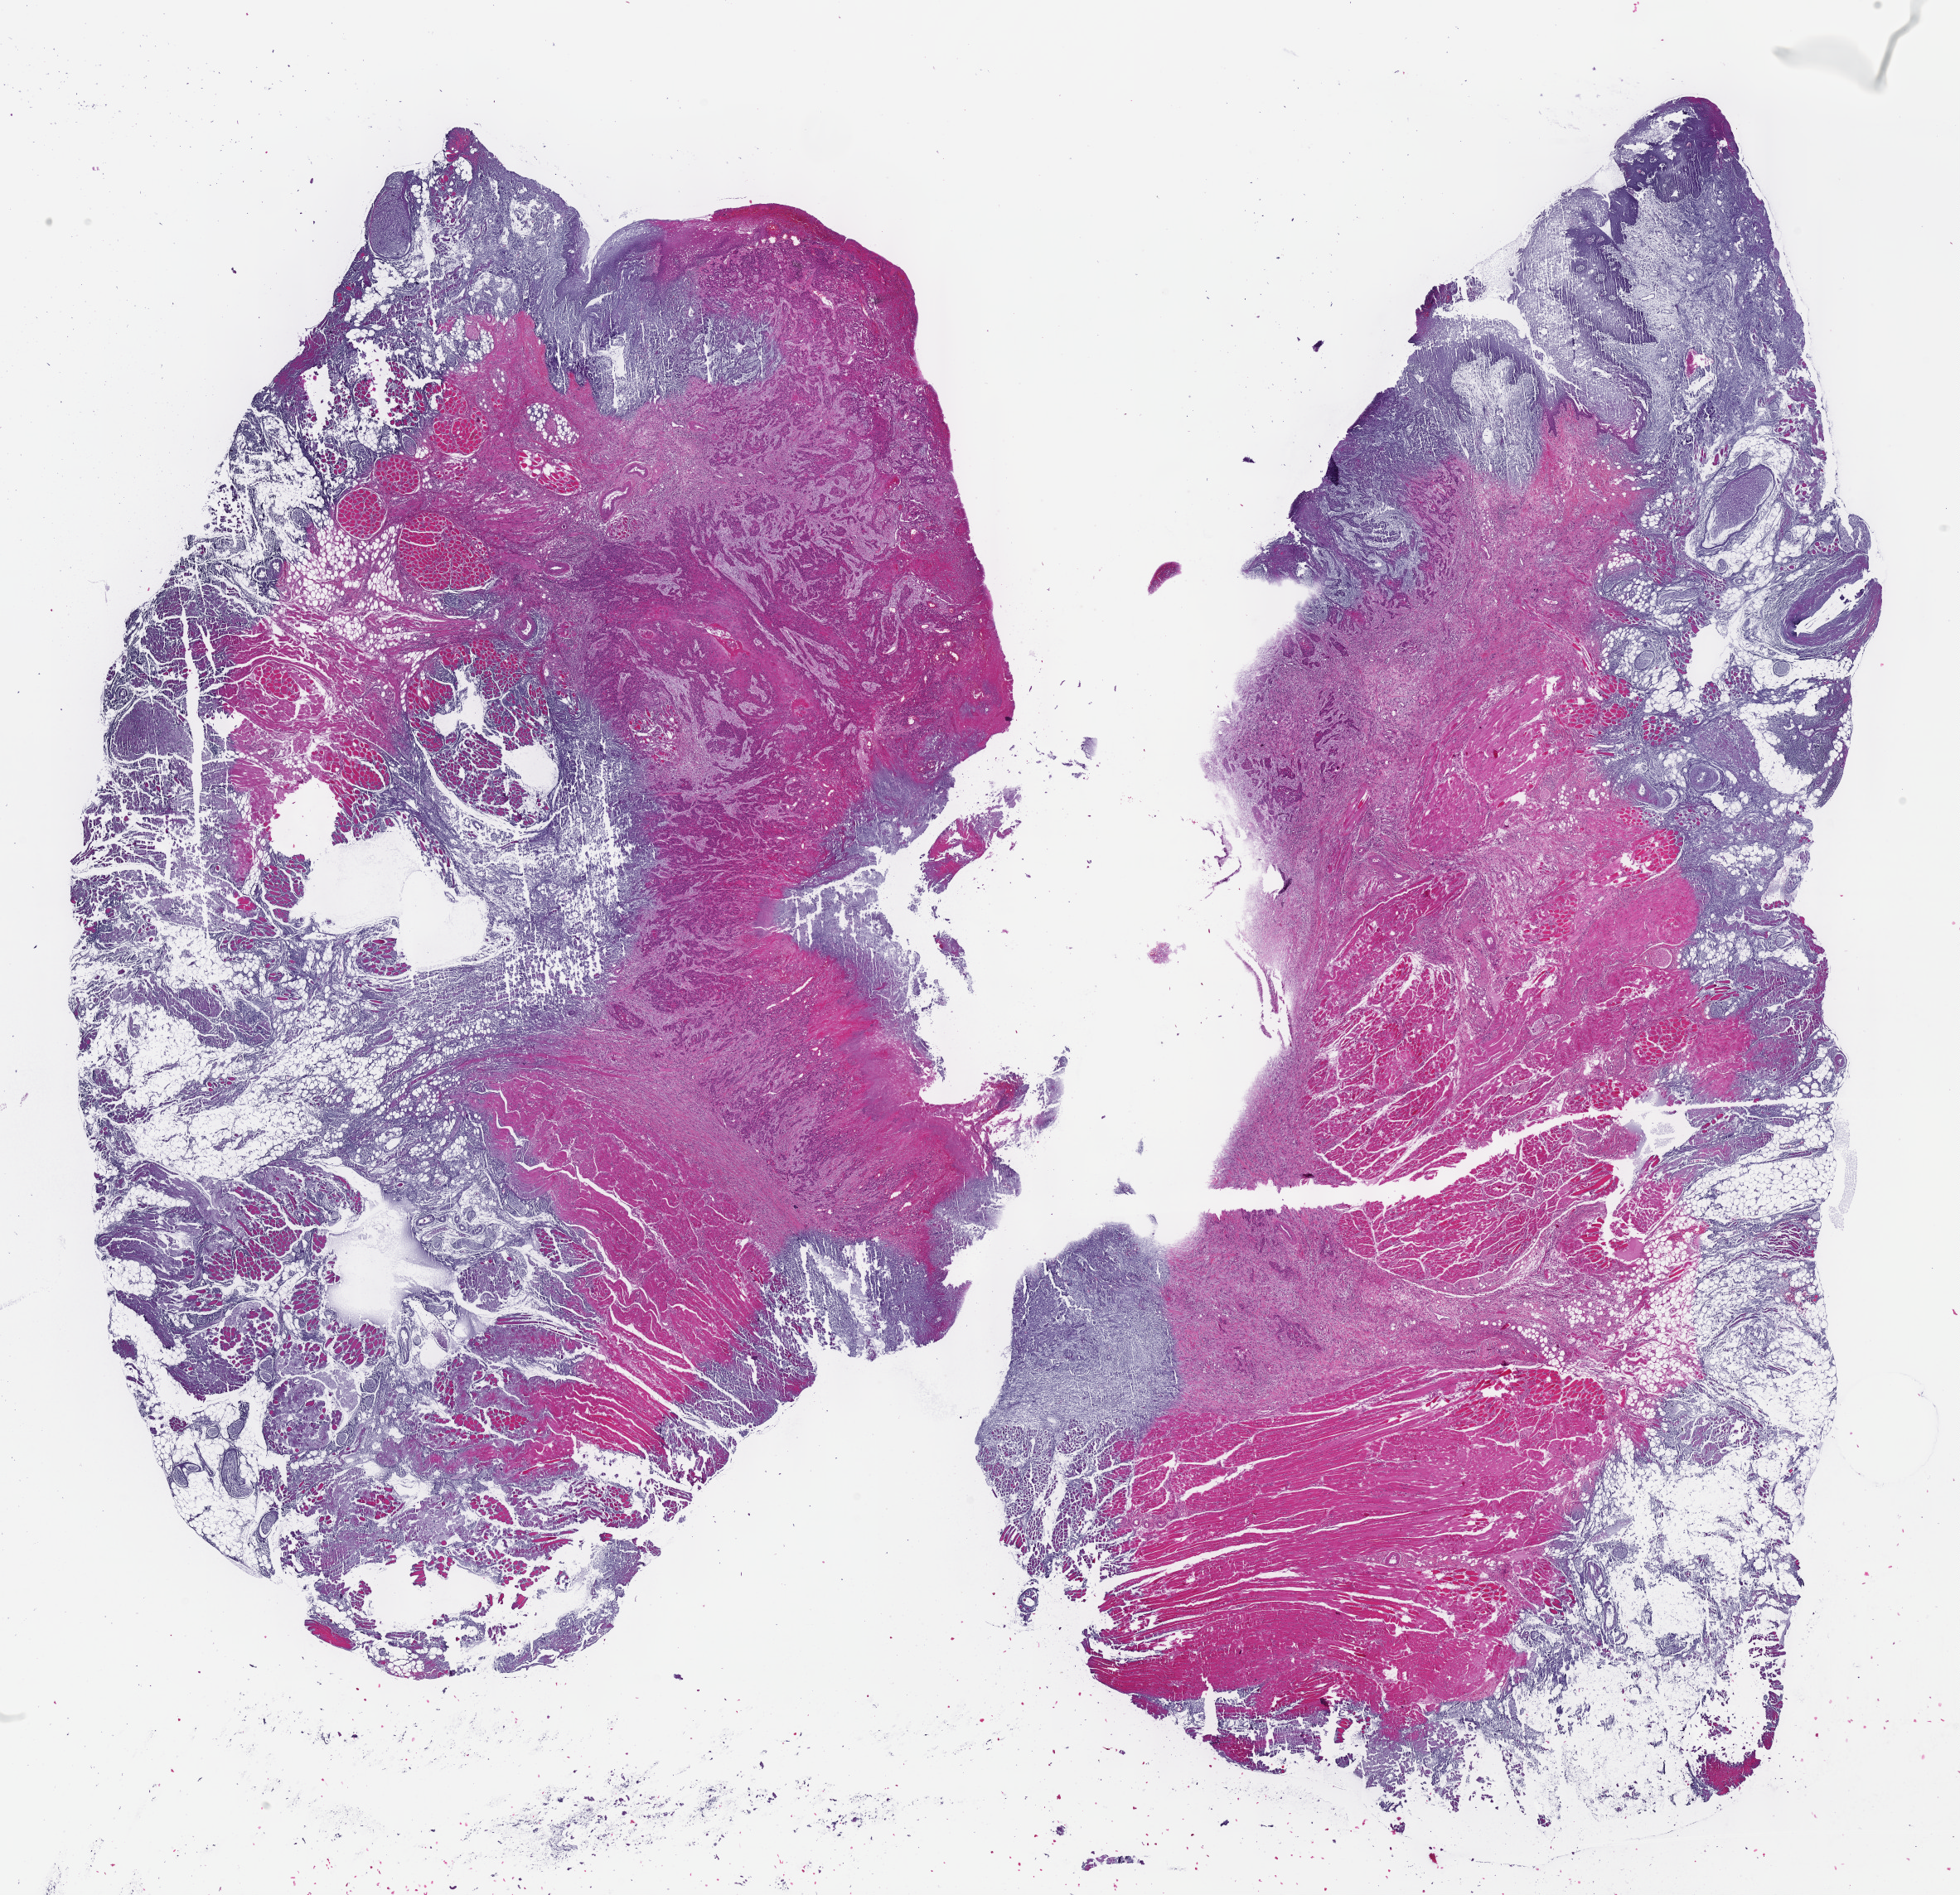
Digitized H&E tissue section (whole slide), a low-resolution overview of the entire scanned area, about 19.1 x 18.5 mm (slide scanned at 40x); formalin-fixed paraffin-embedded (FFPE) diagnostic section; sample: primary tumour, head and neck. Female, age 76 years at initial diagnosis. Histologic grade: G3 (poorly differentiated).
• lymph nodes positive (case pathology): 3 of 24 examined
• AJCC pathologic stage: IVA (7th edition)
• pathologic diagnosis: Squamous cell carcinoma, NOS (floor of mouth, NOS)